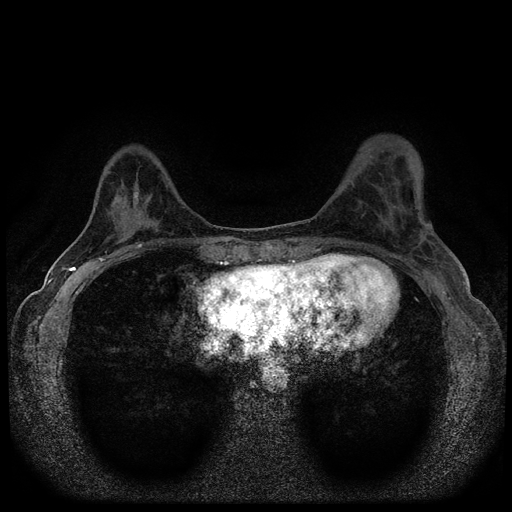
Breast MRI (dynamic contrast-enhanced, multi-phase), one axial slice. Slice 35 of 116 in the series (ordered by position). Dynamic contrast-enhanced series, time point 2 of 5 at this slice position (early post-contrast). 1.5 T. TE 2.7 ms, TR 5.6 ms. 2 mm slice thickness. 512 × 512 image matrix, field of view 310 × 310 mm. Patient: female, 40 years.
Outlined on this slice (semi-automatically segmented with operator editing):
- breast lesion (labelled benign in the annotation): bounding box (x1, y1, x2, y2) in pixels: (130, 188, 149, 231)